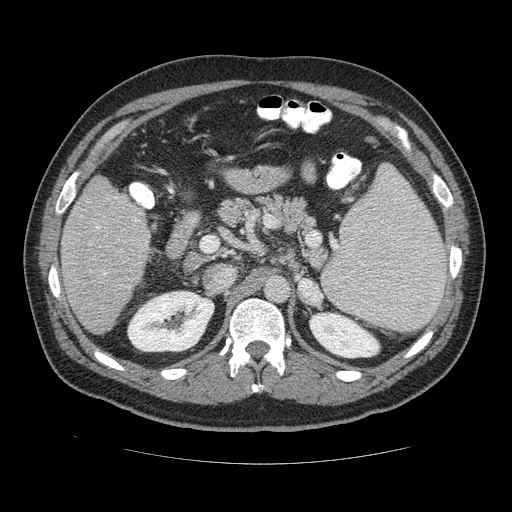
Contrast-enhanced abdominal CT (liver protocol), one axial slice; slice 68 of 113 in the series (ordered by position); reconstruction kernel STANDARD; soft-tissue window (W 400 / L 40 HU); 2.5 mm slice thickness; 512 × 512 image matrix. From the clinical record (not read from this slice): diagnosis: hepatocellular carcinoma (patient treated with transarterial chemoembolisation; whether this scan precedes or follows treatment is not stated here); TNM stage (as recorded): Stage-II; Child-Pugh class: B; tumour differentiation: moderately differentiated; tumour nodularity: multinodular.
Outlined on this slice (semi-automatic segmentation, software-assisted and operator-edited):
- liver parenchyma outside the tumour (the mass and vessels are separate outlines, so this box may not span the whole liver): bounding box <59,173,152,336> (left, top, right, bottom; pixels)
- liver vessels: <96,226,106,276>